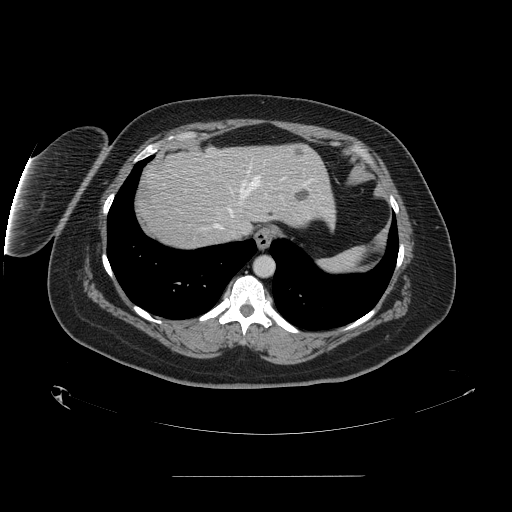
Contrast-enhanced abdominal CT, one axial slice. Slice 131 of 164 in the series (ordered by position). Intravenous contrast given. Soft-tissue window (W 400 / L 40 HU). 2.5 mm slice thickness. 512 × 512 image matrix. Female patient, age 52 years. Case-level facts recorded for this patient, not image findings: diagnosis: colorectal cancer liver metastases, imaged before liver resection; multiple liver metastases: yes; largest metastasis: 3.5 cm; disease in both lobes: no.
Outlined on this slice (outlined manually by an expert reader):
- hepatic veins: box from (x=214, y=167) to (x=286, y=237) px
- liver: (x=142, y=144)–(x=334, y=250)
- planned liver remnant (the part of the liver to remain after resection): (x=173, y=144)–(x=334, y=229)
- liver metastasis: (x=295, y=190)–(x=309, y=202)
- liver metastasis: (x=266, y=209)–(x=275, y=218)
- liver metastasis: (x=297, y=151)–(x=303, y=155)